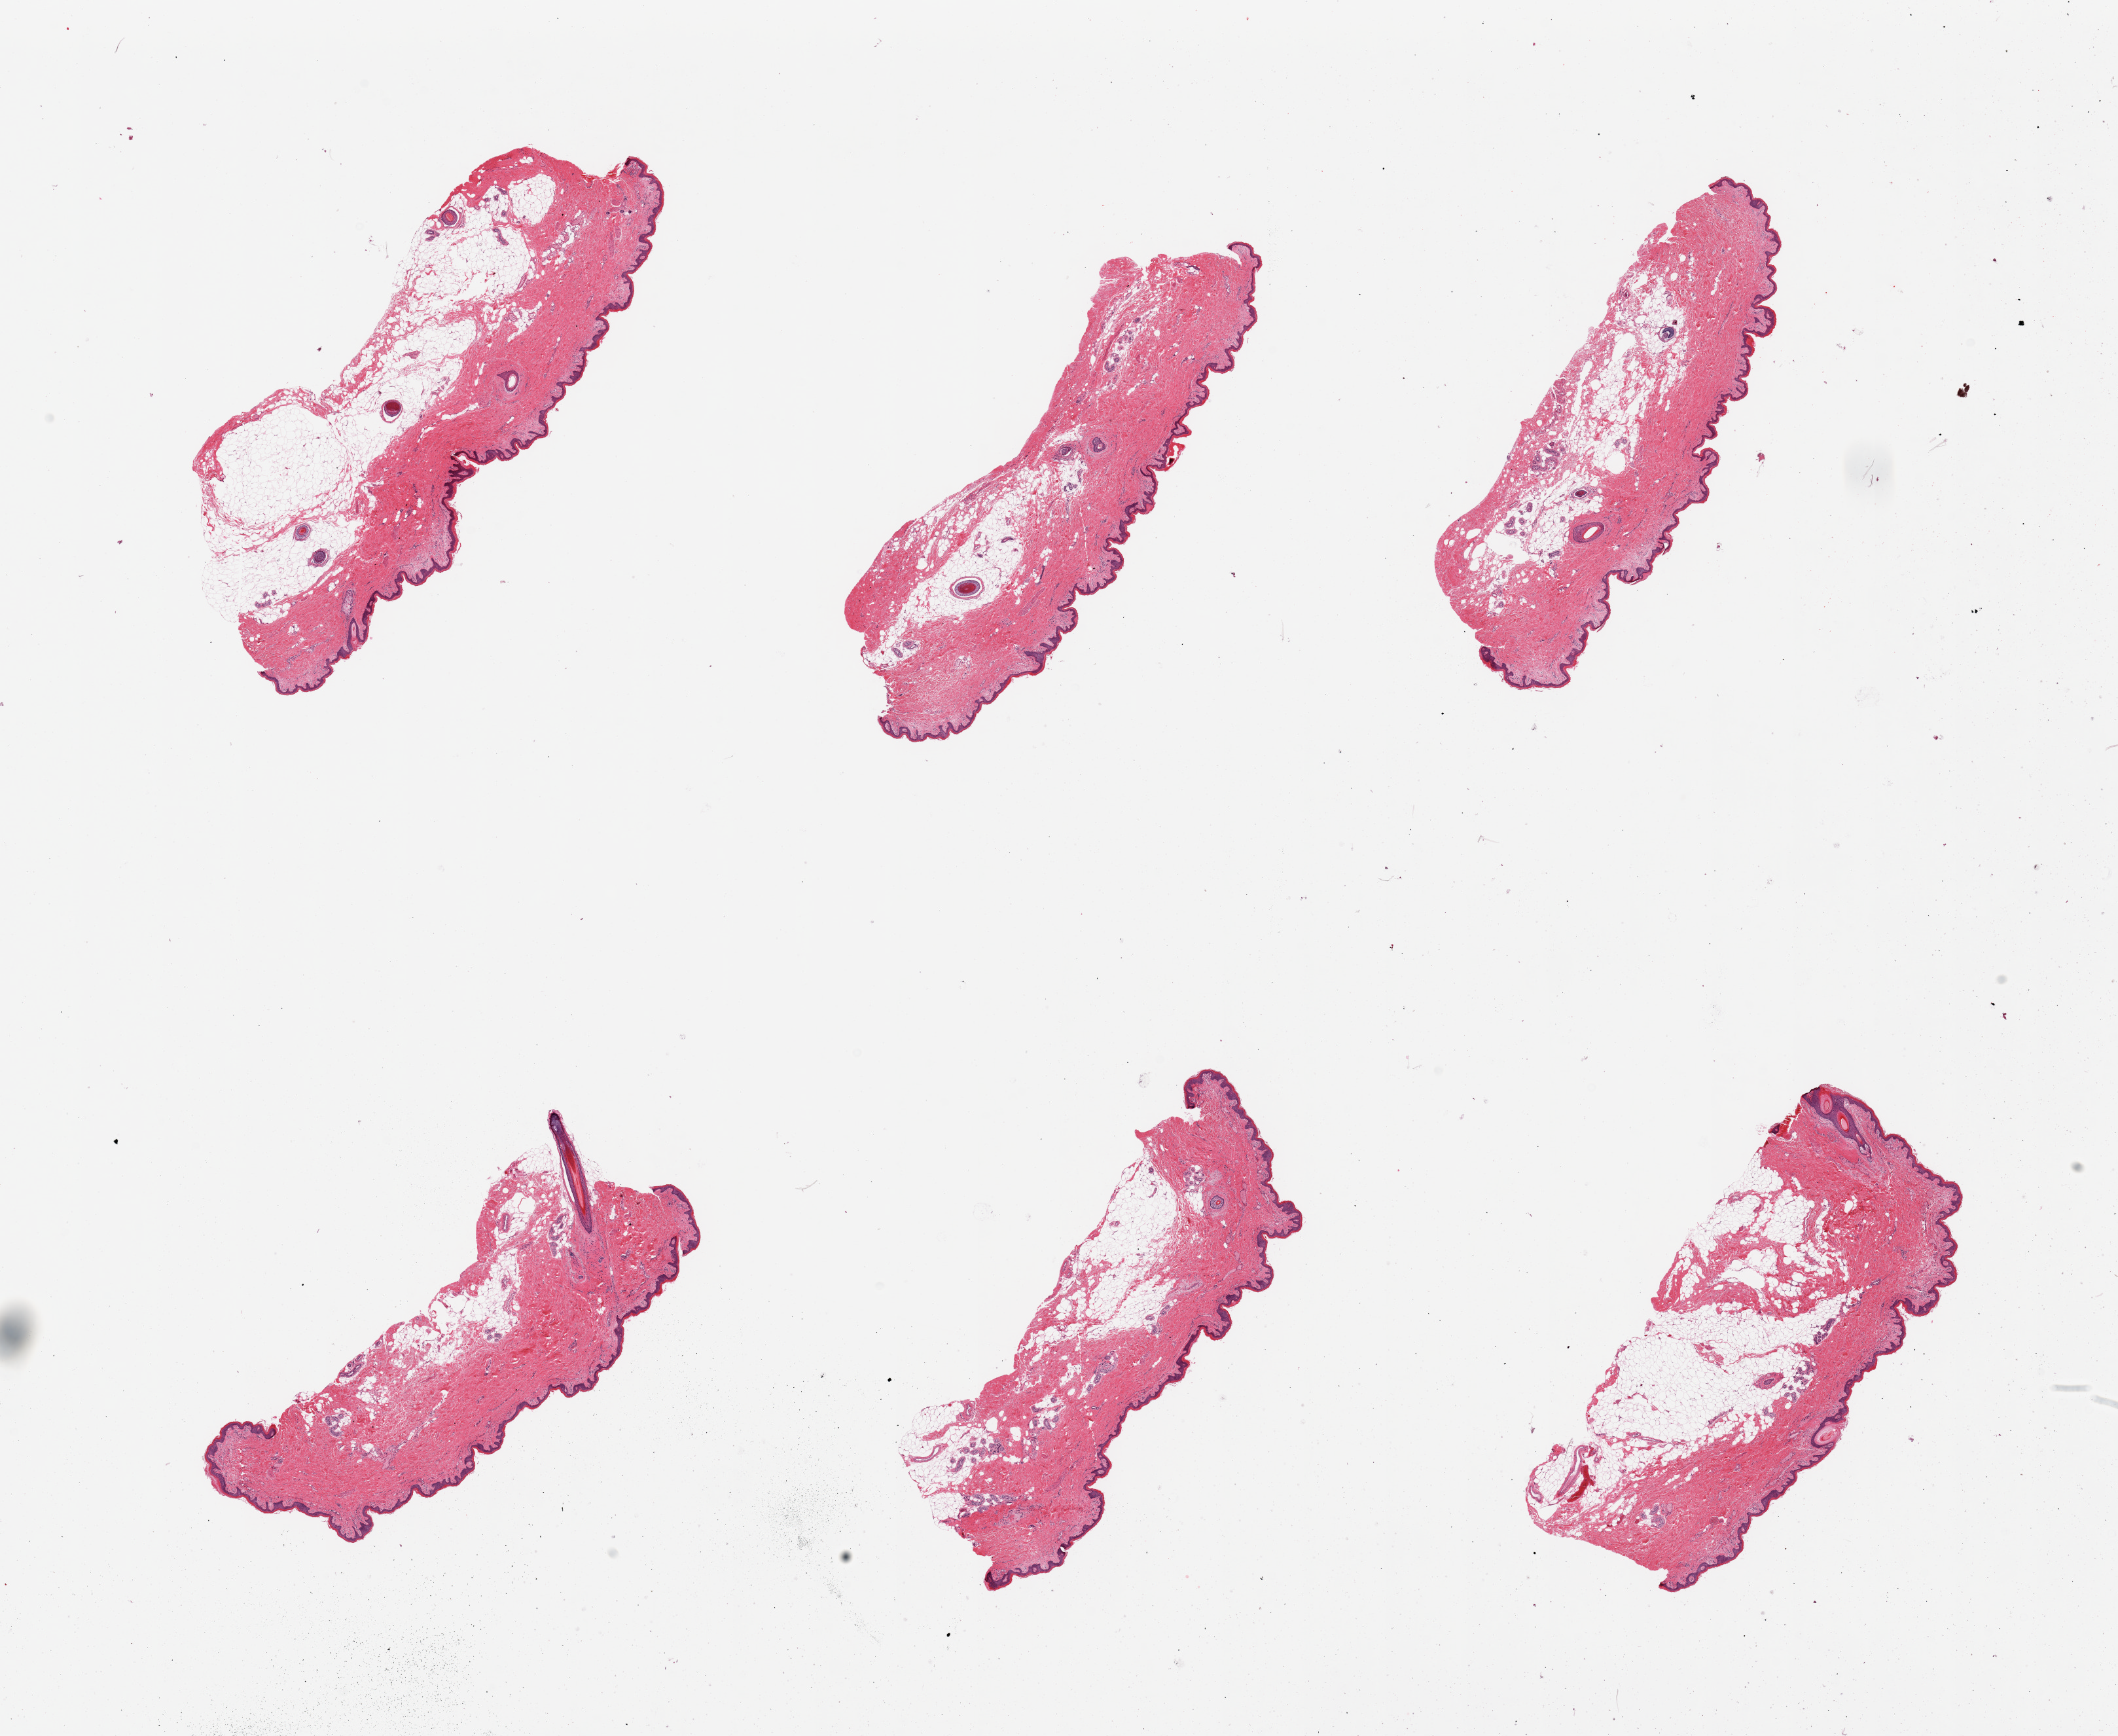
Hematoxylin and eosin (H&E) whole-slide image, shown as a low-resolution overview of the whole scanned area (about 25.6 x 21.0 mm); PAXgene-fixed, paraffin-embedded tissue; sampled site (target tissue): skin of suprapubic region; tissue donor sample. Donor: female.
Review note (as recorded): 6 pieces, range from 10-50% adipose tissue (internal and attached).